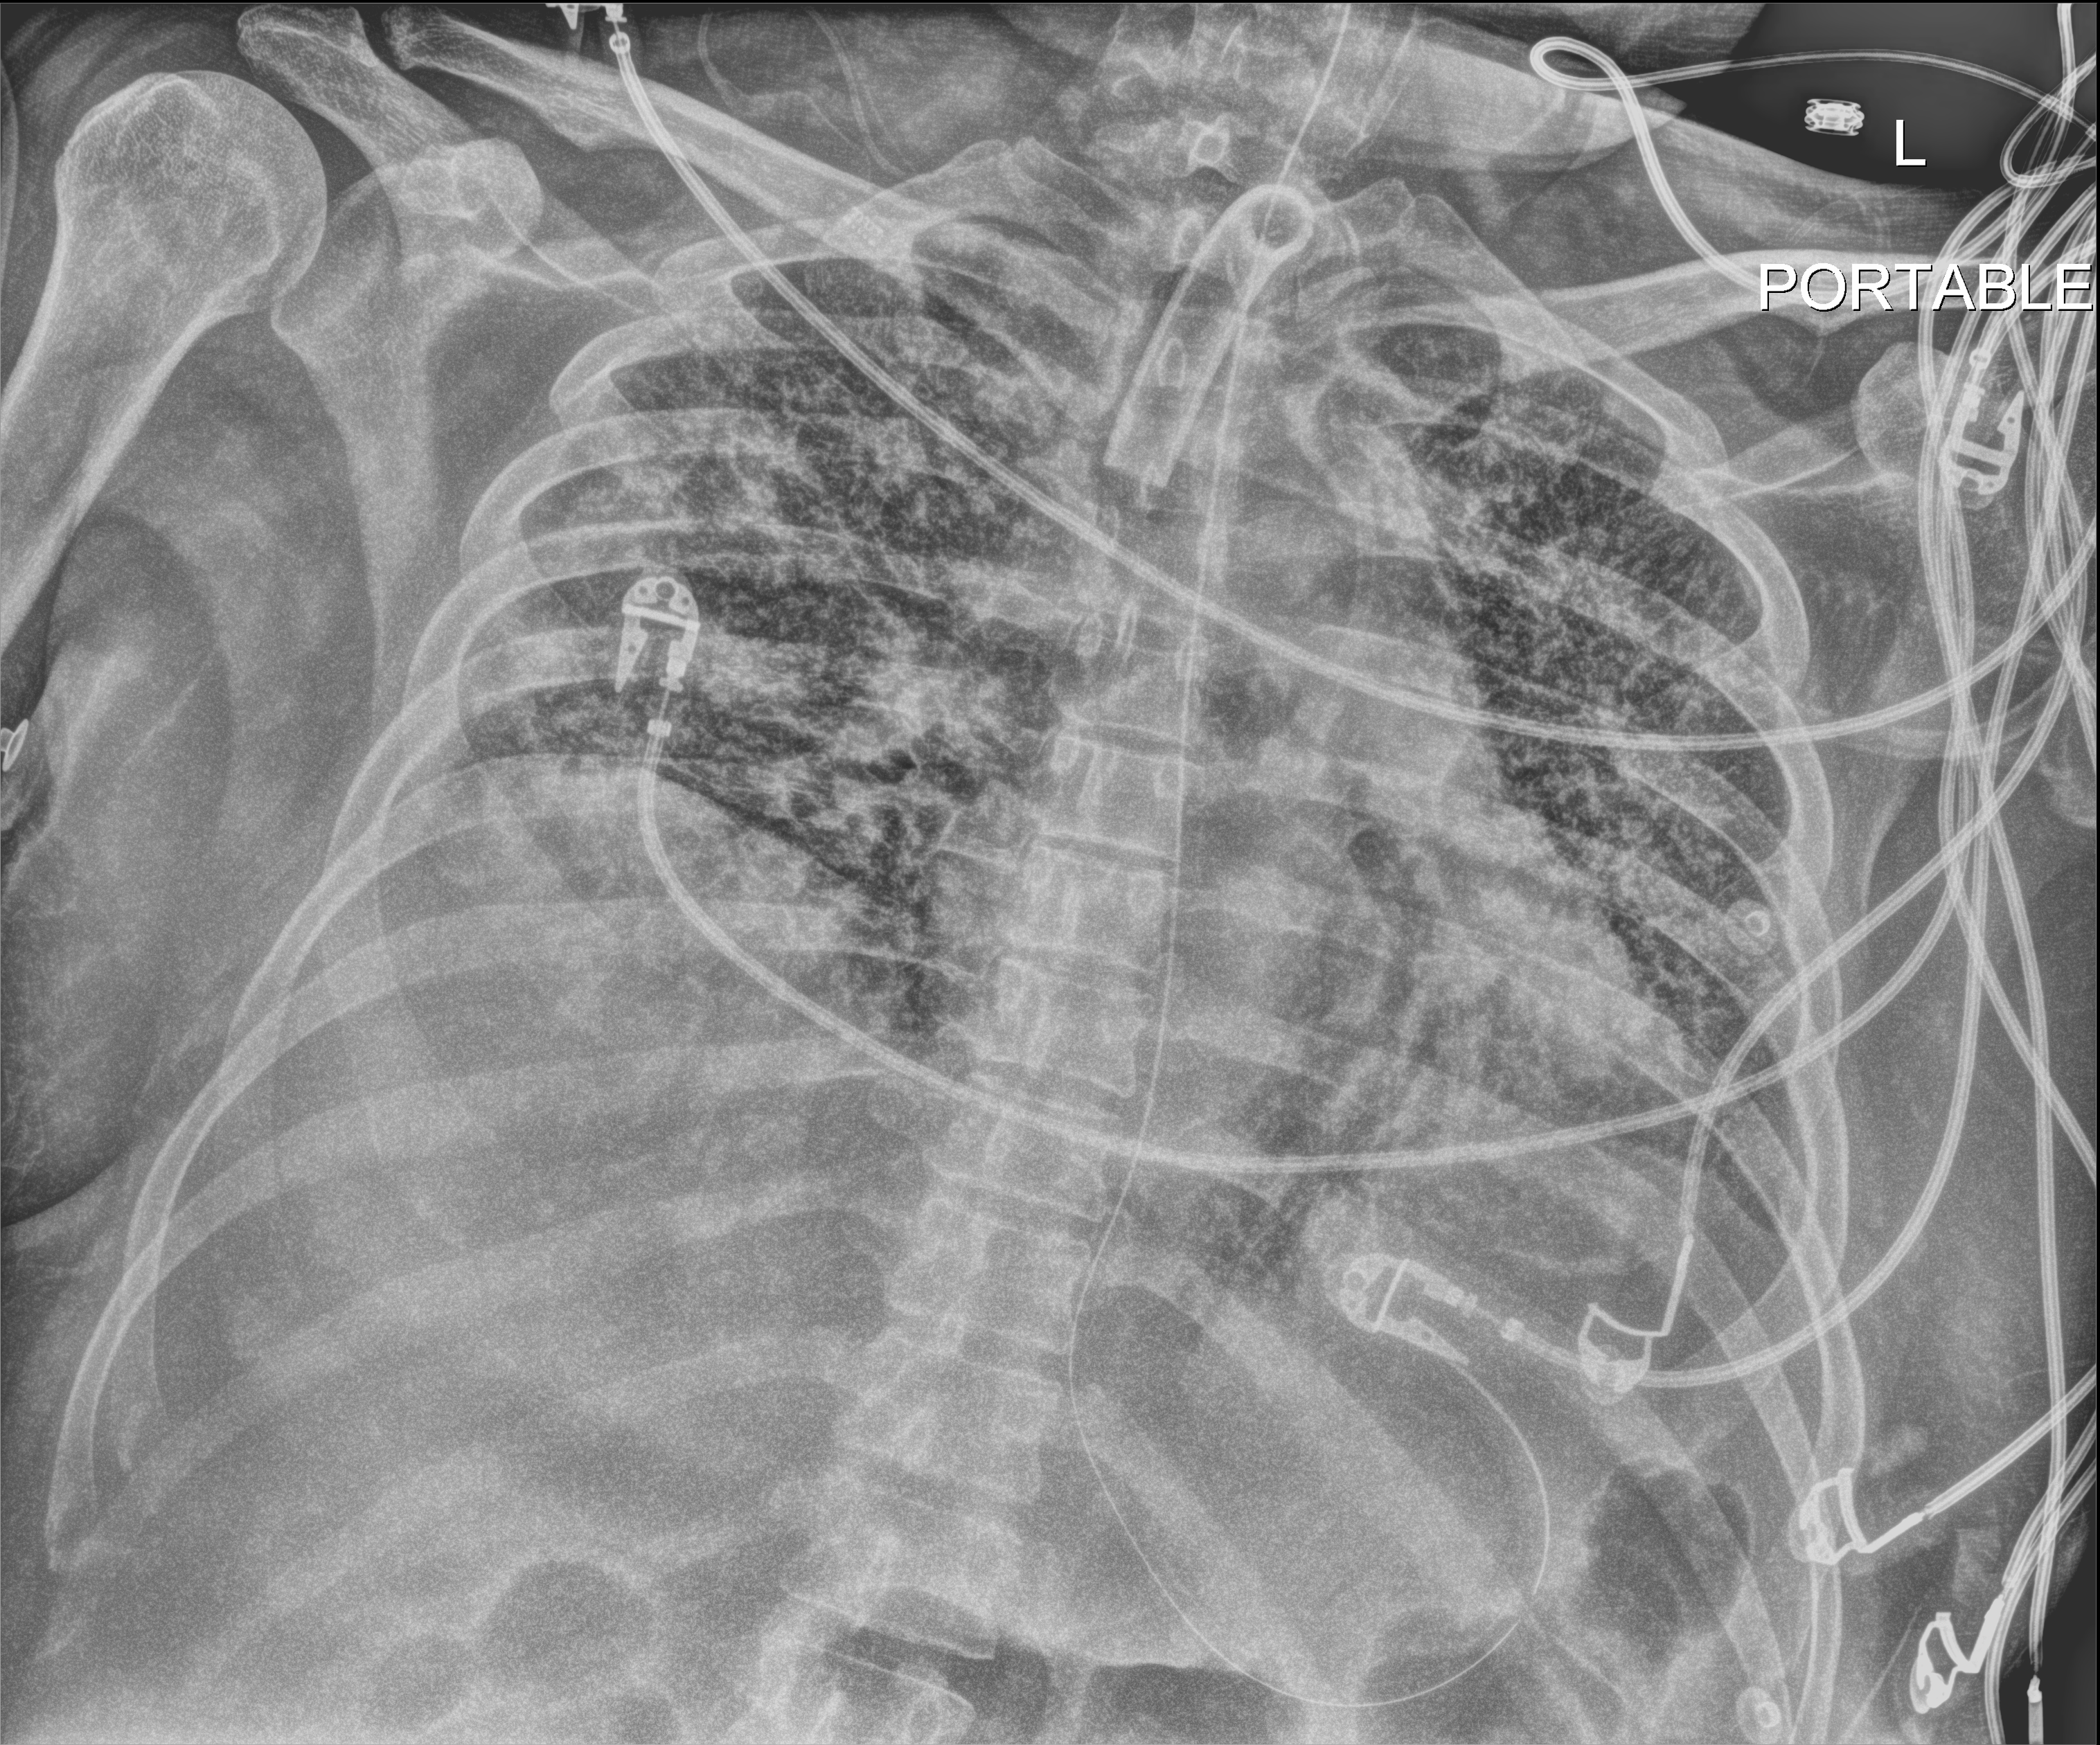
Bedside chest radiograph (digital radiography); anteroposterior (AP) projection. Patient hospitalised with COVID-19; male, aged 18–59 years.
Admission-level facts for this patient (not findings on this image; timing relative to this image not recorded): chronic kidney disease (admission record): no; admitted to intensive care during this hospital stay: yes; mechanically ventilated during this hospital stay: yes.